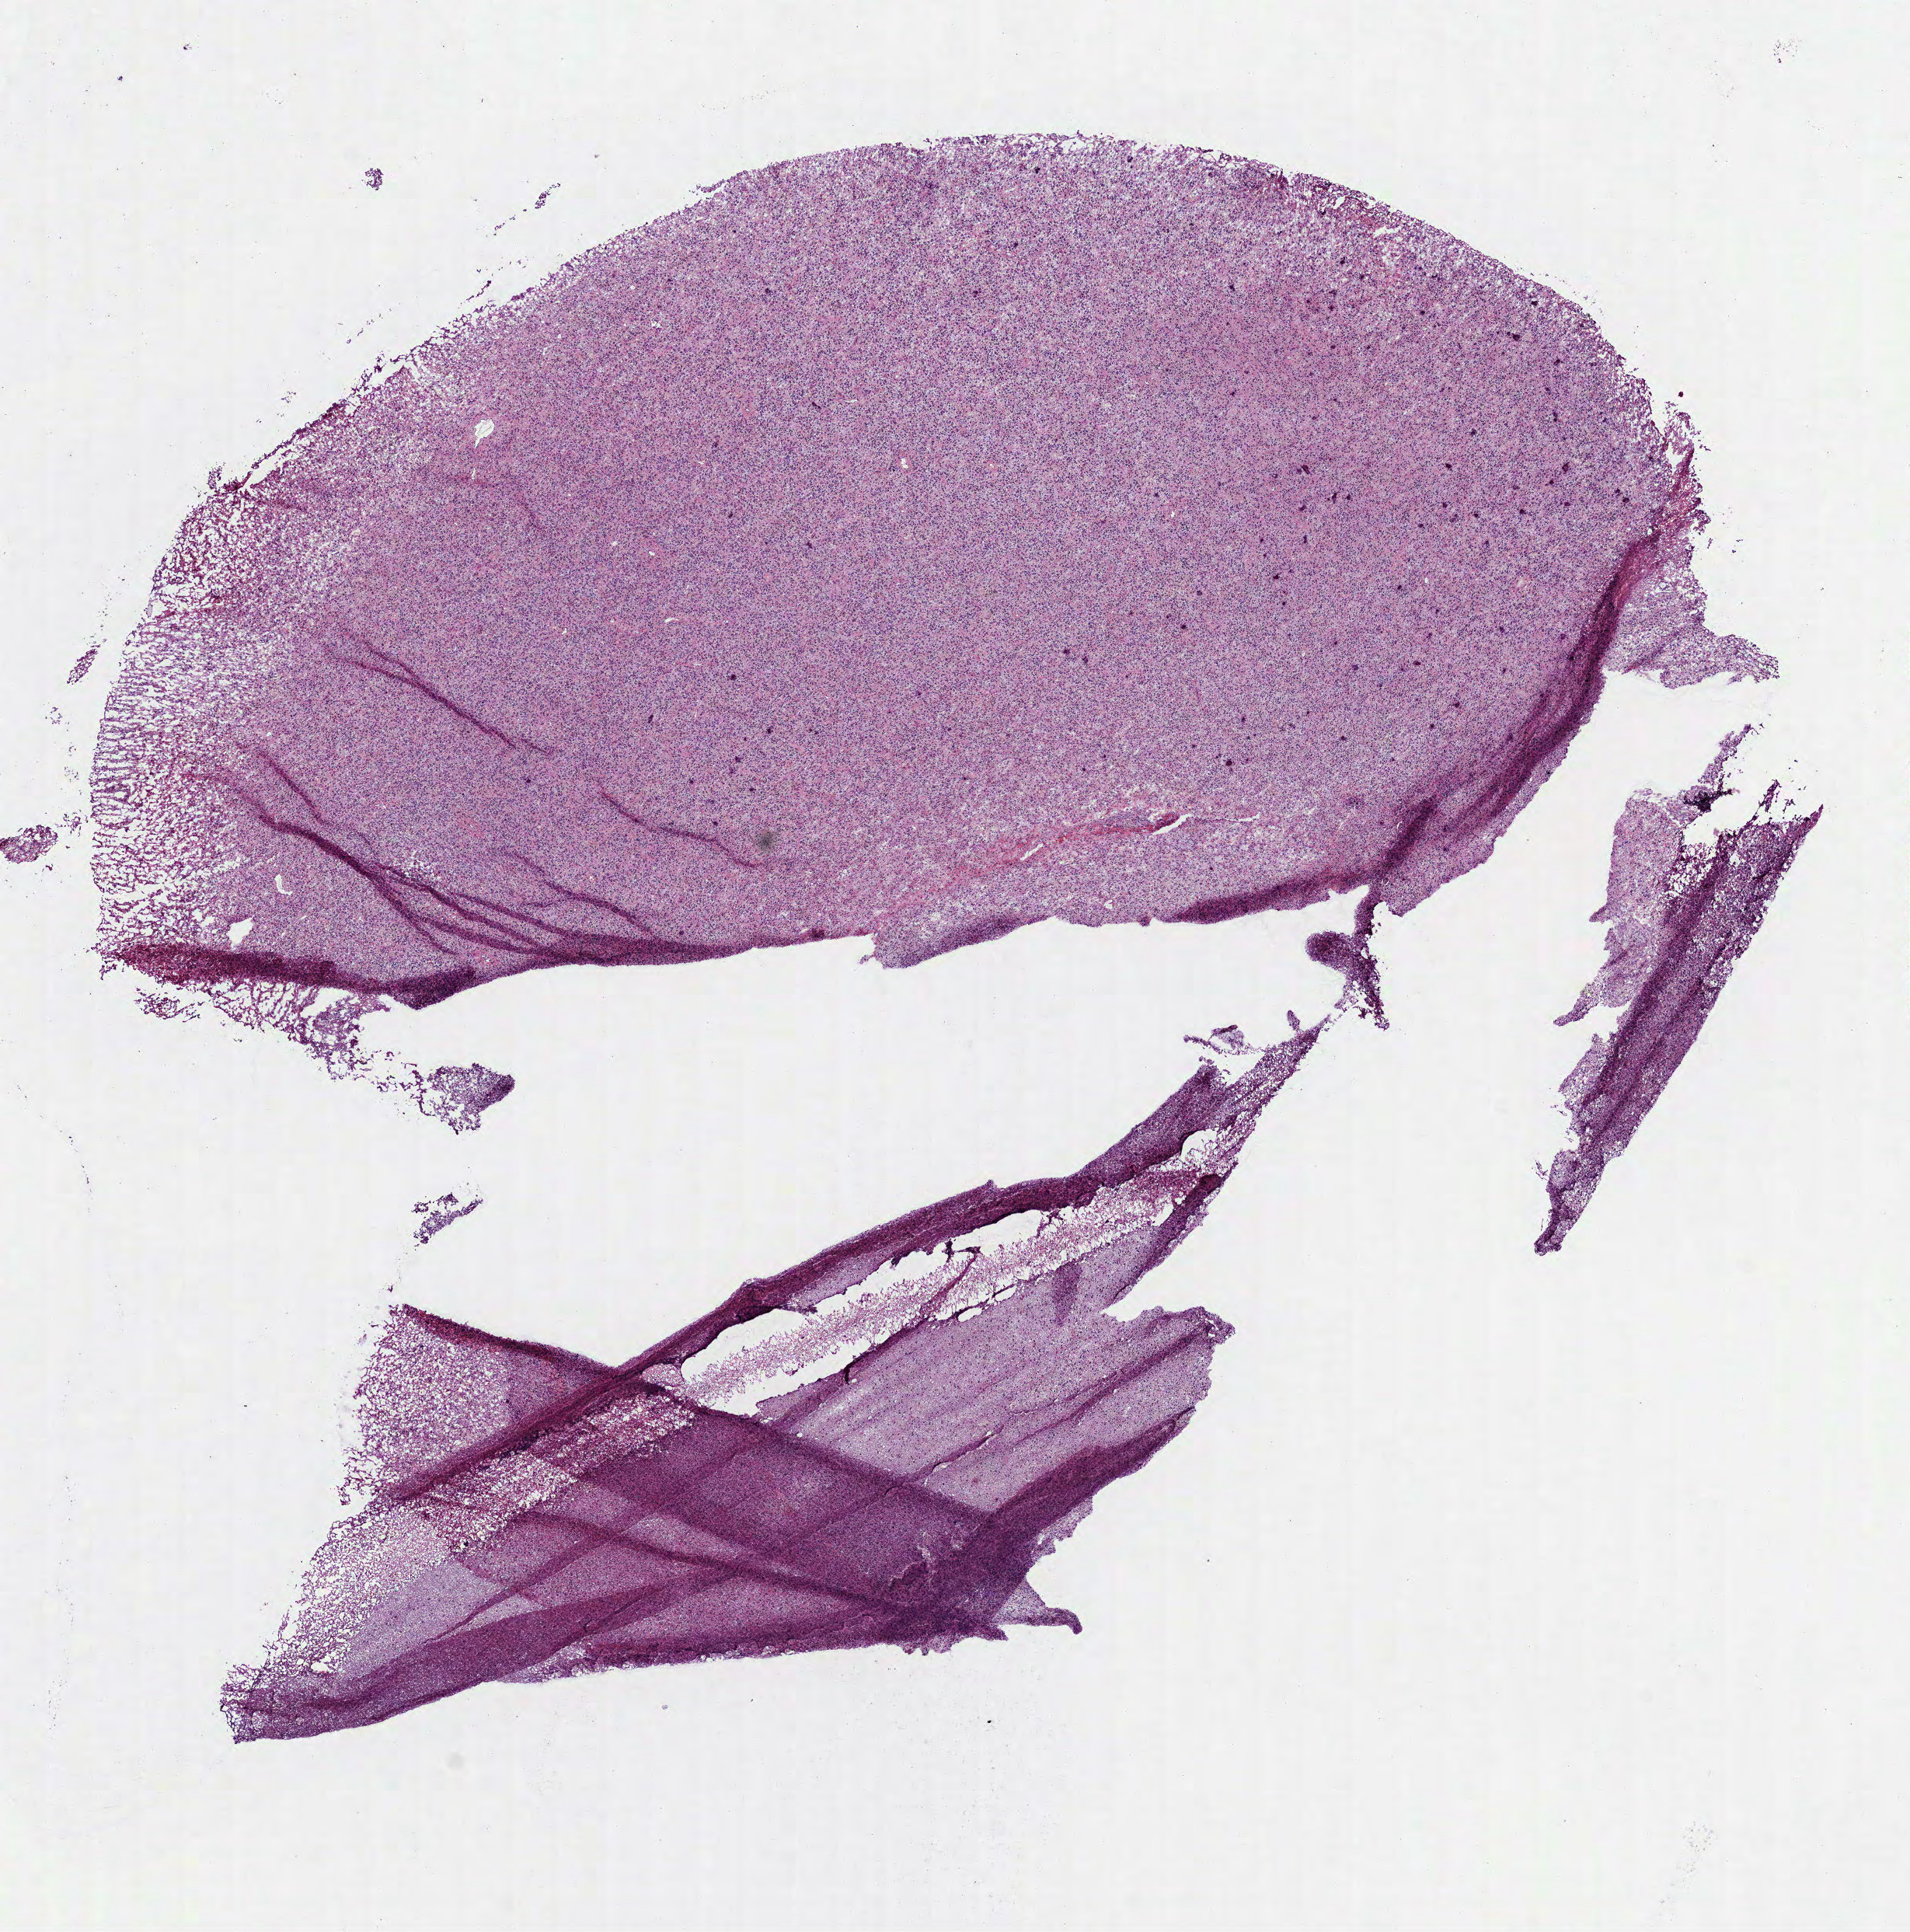
Digitized H&E tissue section (whole slide), whole scanned area (about 9.9 x 10.0 mm, from a 40x scan) shown as a low-resolution overview. Frozen section from the bottom of the tissue portion. Primary tumour sample from the brain. Patient: male, age at initial diagnosis 59 years. Histologic grade: G3 (poorly differentiated). Slide review estimates, as recorded: tumour cells 100%, tumour nuclei 80%, normal cells 0%, stromal cells 0%, necrosis 0%.
• diagnosis: Astrocytoma, anaplastic (cerebrum)
• laterality: left